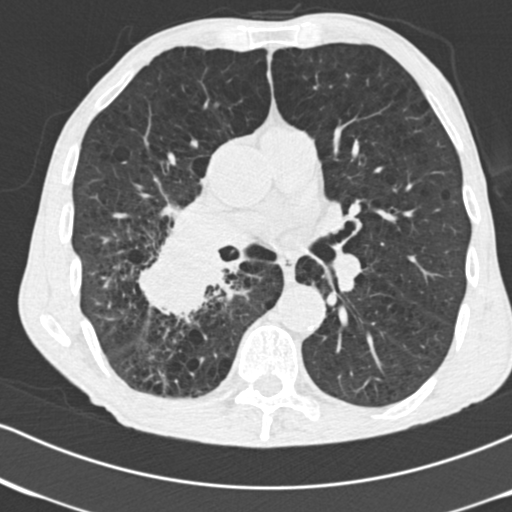
Low-dose screening chest CT, one axial slice. Lung window (W 1500 / L -600 HU). 2 mm slice thickness. 512 × 512 image matrix, field of view 316 × 316 mm.
Structures marked on this image (manually delineated by an expert):
- lesion 1 (tumor, lower lobe of right lung): box from (x=139, y=217) to (x=224, y=316) px